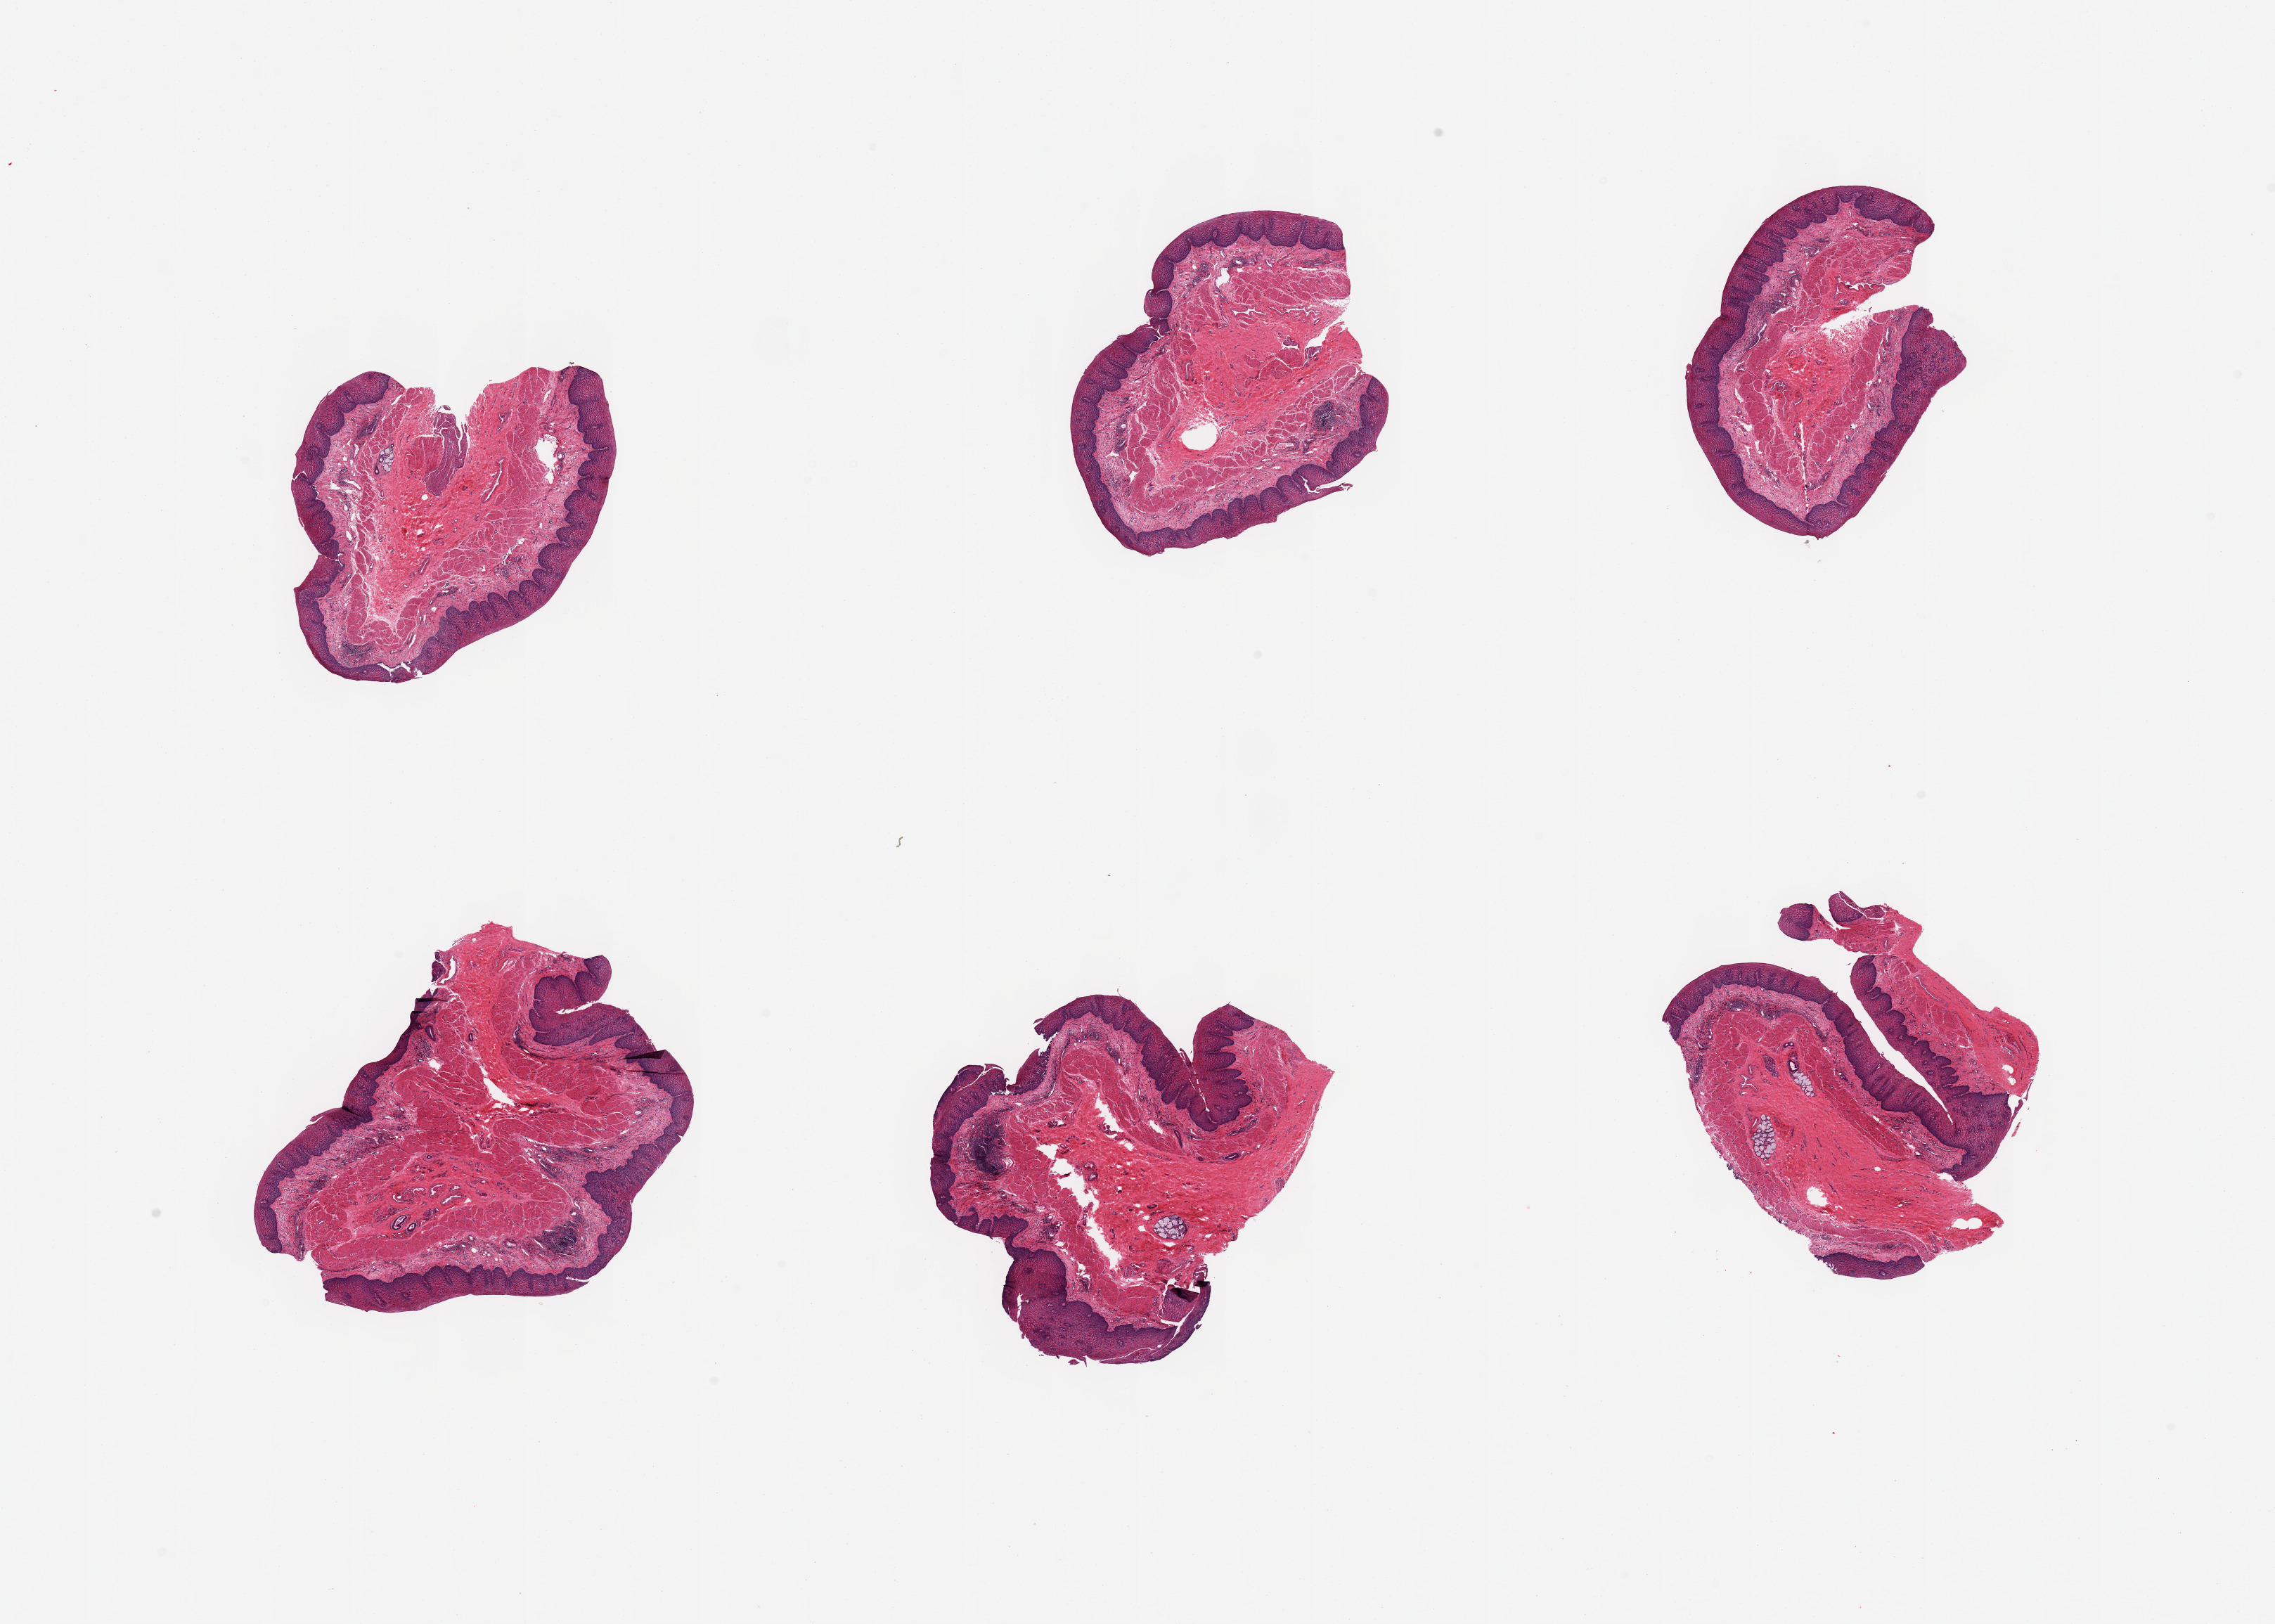
Digitized haematoxylin and eosin-stained section, low-resolution overview of the scanned area, about 25.6 x 18.3 mm (slide scanned at 20x); PAXgene-fixed paraffin-embedded (PFPE) section; target tissue: esophageal mucous membrane; donor tissue sample. Donor: female.
Pathologist's review note for this sample: 6 pieces, squamous mucosa up to ~0.4mm; ~15-20% thickness; incidental submucosal mucus glands.